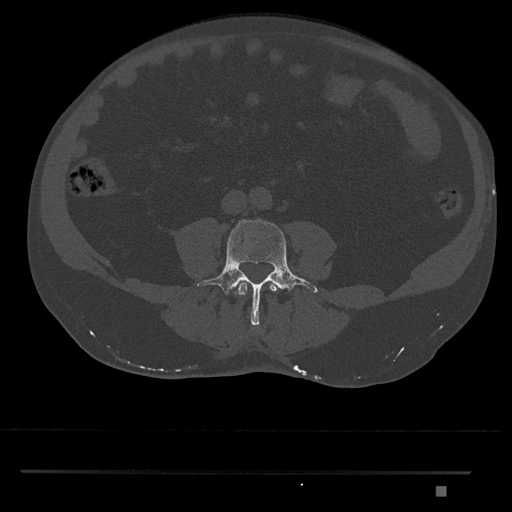
CT including the spine, one axial slice. 120 kVp. Bone window (W 1800 / L 400 HU). 0.5 mm slice thickness. 512 × 512 image matrix. Male patient, age 65 years. From the clinical record (not read from this slice): primary cancer: prostate.
Structures marked on this image (semi-automatically segmented with operator editing):
- L3 vertebra: bounding box [x1, y1, x2, y2] px = [235, 281, 279, 296]
- L4 vertebra: [197, 218, 318, 326]